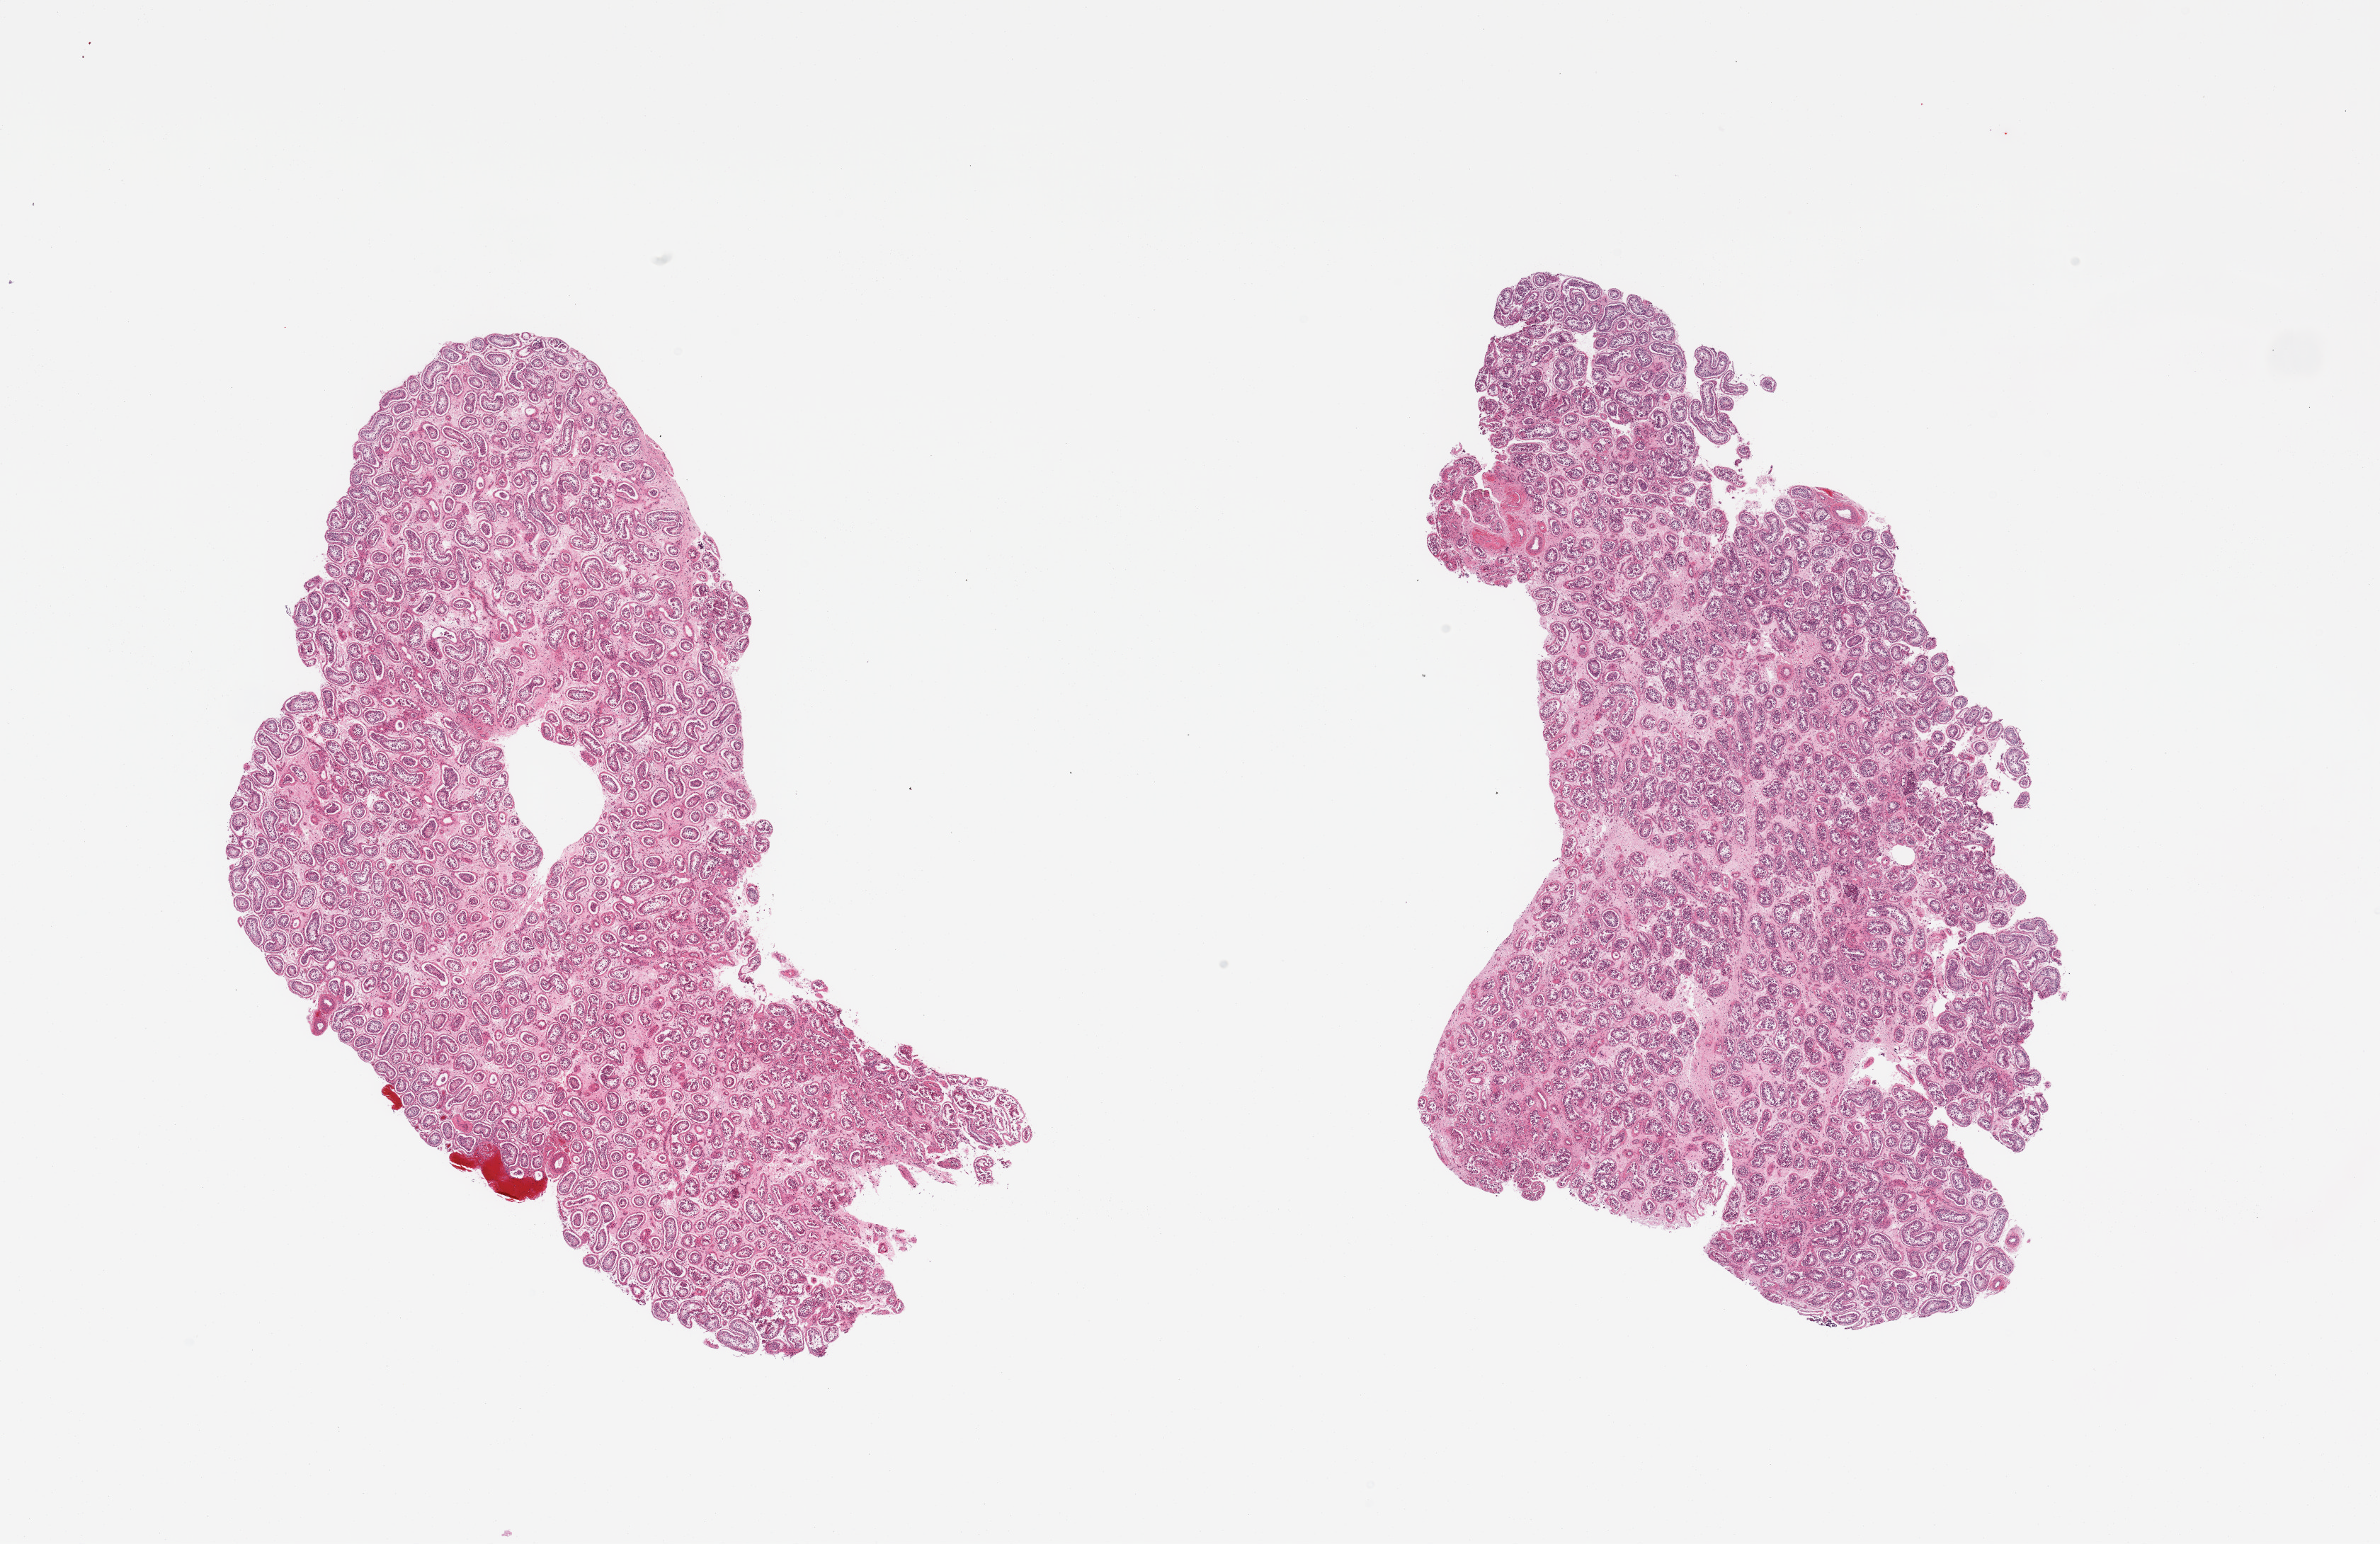
Digitized haematoxylin and eosin-stained section, brightfield — whole scanned area (about 26.6 x 17.2 mm) shown as a low-resolution overview; PAXgene-fixed paraffin-embedded (PFPE) section; sampled site (target tissue): testis; tissue donor sample. Donor sex: male.
Reviewer comment on this tissue sample: 2 pieces; decreased spermatogenesis and predominance of Sertolii cells.